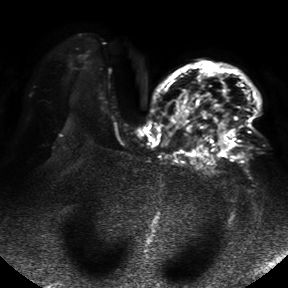
Breast MRI, one axial slice; slice 30 of 50 in the series (ordered by position); diffusion-weighted series; image 2 of 4 stored at this slice position (different b-values; order by instance number); 1.5 T; 4 mm slice thickness; 288 × 288 image matrix, field of view 390 × 390 mm. Female patient.
Annotated regions visible in this slice (manually delineated by an expert):
- tumour on diffusion-weighted imaging: bounding box (x1, y1, x2, y2) in pixels: (219, 124, 235, 155)